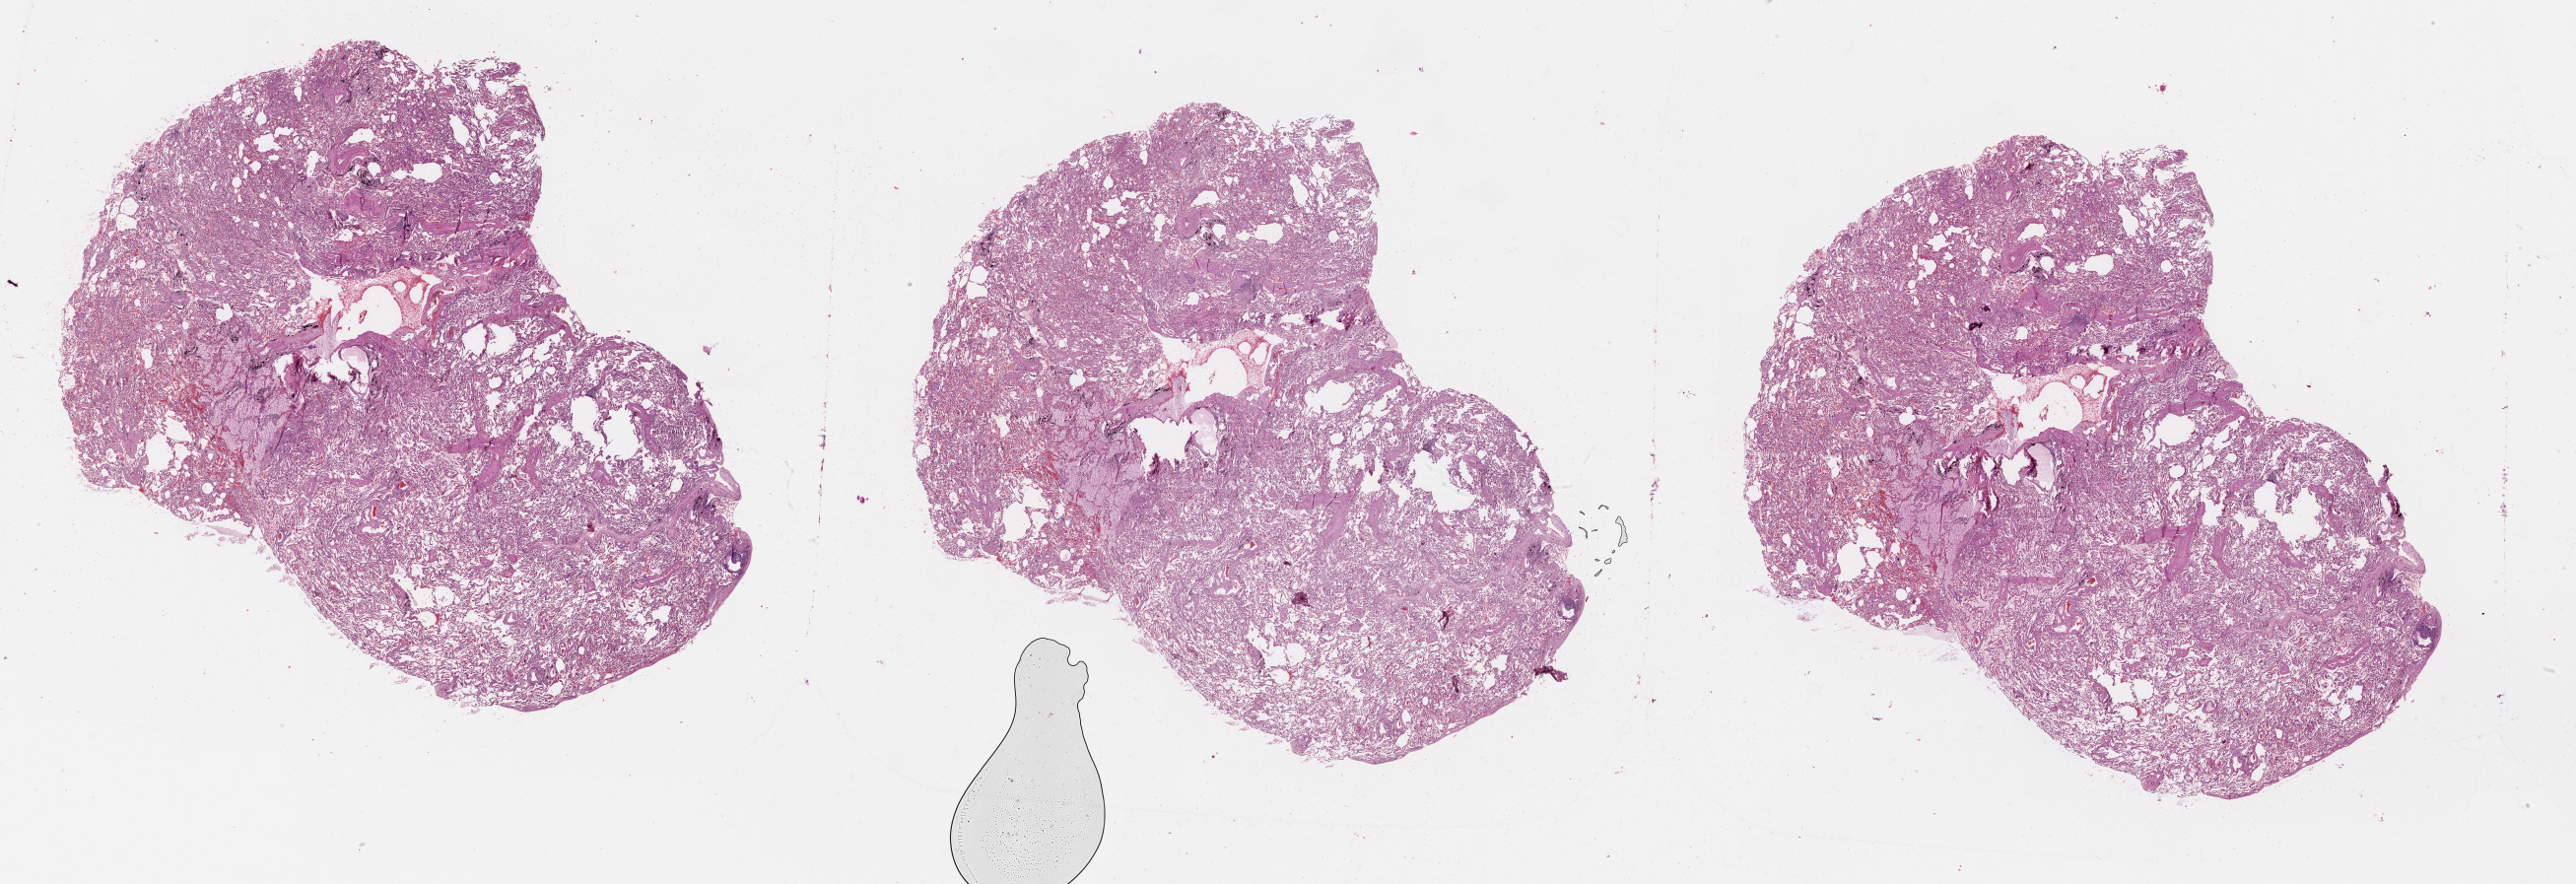
Digitized H&E tissue section (whole slide) — a low-resolution overview of the entire scanned area, about 42.1 x 14.4 mm; lung, normal (non-tumour) tissue. 71-year-old male patient.
This section: normal (non-tumour) tissue from the same patient. Patient diagnosis (cohort enrolment): squamous cell carcinoma (lung).